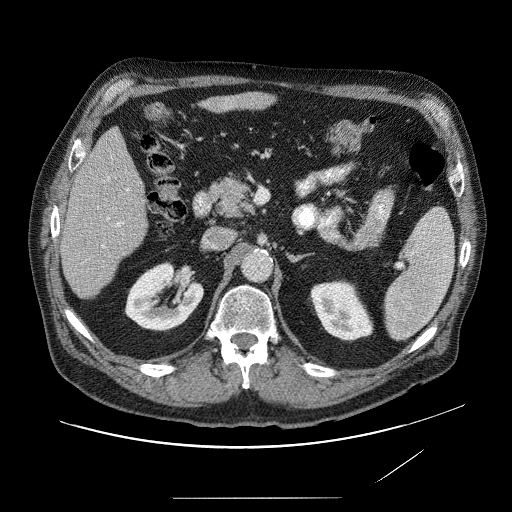
Contrast-enhanced abdominal CT (liver protocol), one axial slice. Slice 29 of 89 in the series (ordered by position). Reconstruction kernel STANDARD. 120 kVp. Soft-tissue window (W 400 / L 40 HU). 2.5 mm slice thickness. 512 × 512 image matrix, field of view 420 × 420 mm. From the clinical record (not read from this slice): diagnosis: hepatocellular carcinoma (patient treated with transarterial chemoembolisation; whether this scan precedes or follows treatment is not stated here); TNM stage (as recorded): Stage-IVA; Child-Pugh class: A.
Annotated regions visible in this slice (semi-automatic segmentation, software-assisted and operator-edited):
- liver parenchyma outside the tumour (the mass and vessels are separate outlines, so this box may not span the whole liver): bounding box (x1, y1, x2, y2) in pixels: (60, 134, 154, 304)
- liver vessels: (99, 169, 135, 253)